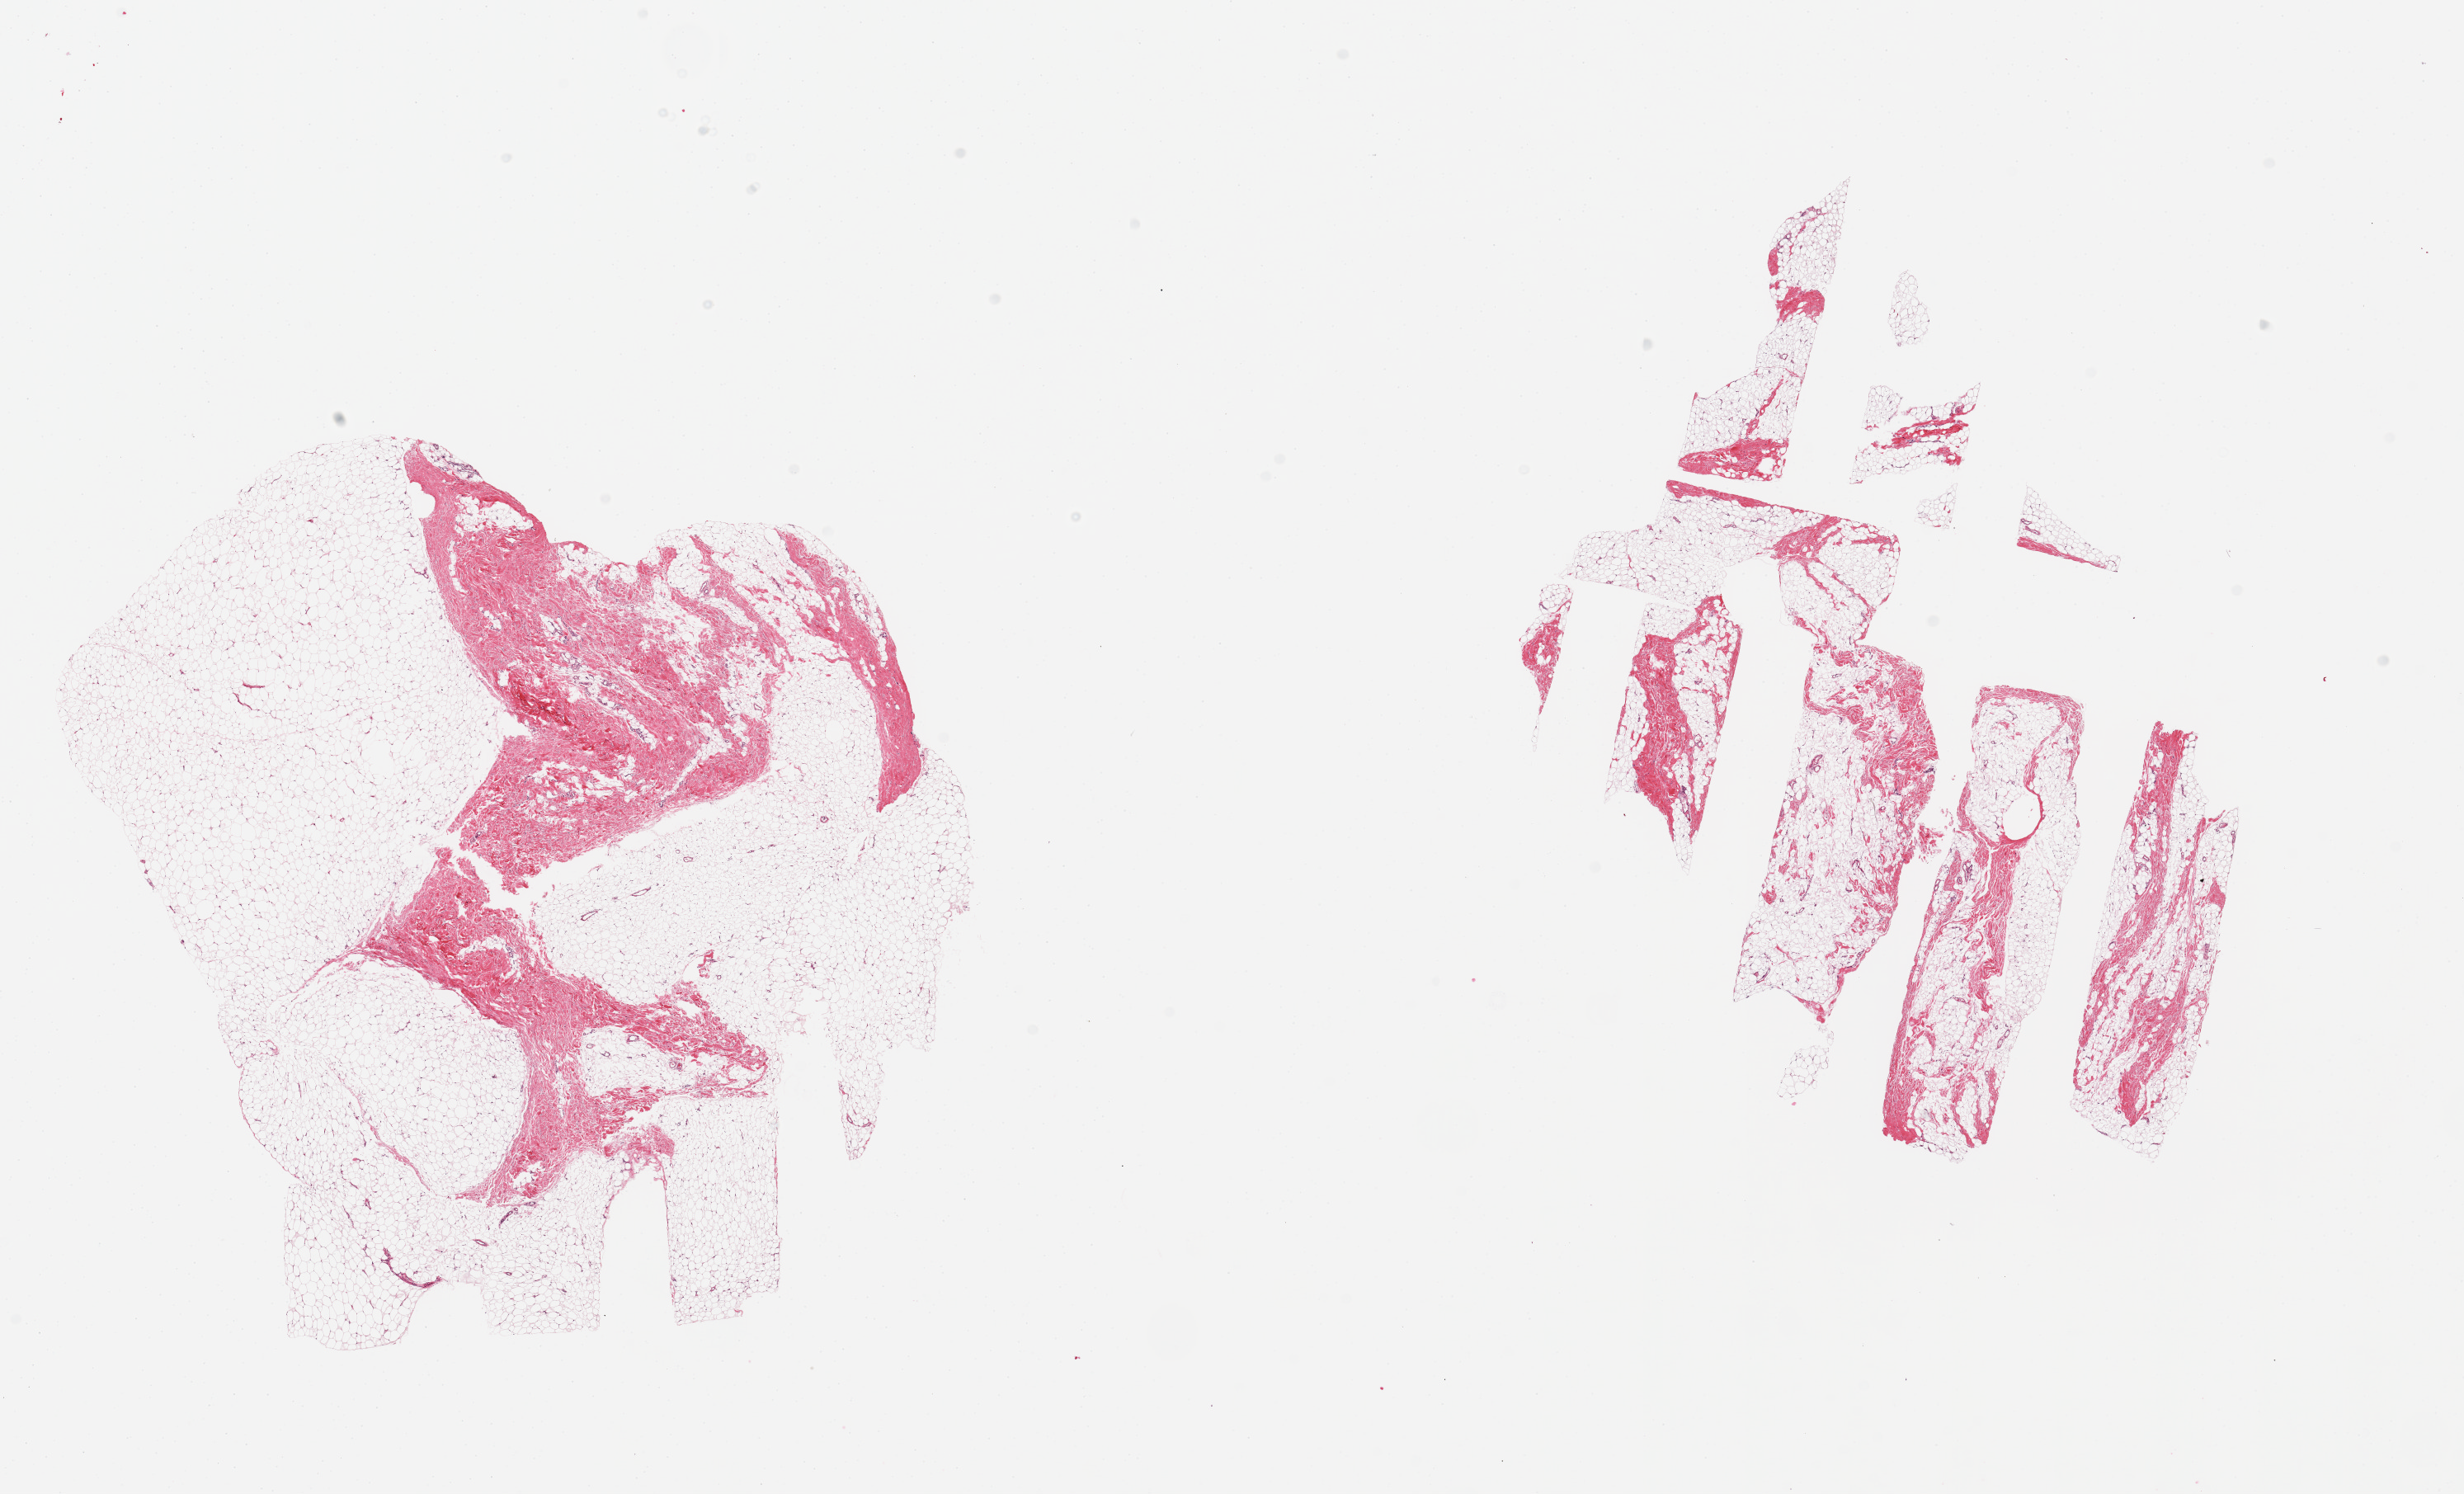
Hematoxylin and eosin (H&E) whole-slide image, brightfield — a low-resolution overview of the entire scanned area, about 23.6 x 14.3 mm (slide scanned at 20x); PAXgene-fixed, paraffin-embedded tissue; sampled site (target tissue): breast; donor tissue sample. Donor sex: male.
Reviewer comment on this tissue sample: 2 pieces, fibroadipose tissue, no ductal elements.